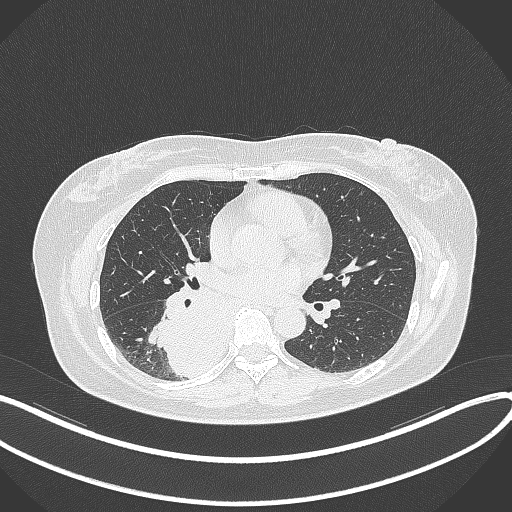
Chest CT, one axial slice; position 178 of 331 along the scan axis; reconstruction kernel B70f; 120 kVp; lung window (W 1500 / L -600 HU); 1 mm slice thickness; 512 × 512 image matrix, field of view 400 × 400 mm. Female patient, age 54 years. Case-level facts recorded for this patient, not image findings: clinical TNM (as recorded): T4 N0 M0.
Structures marked on this image (bounding box drawn by a radiologist):
- lung tumour (recorded histology: adenocarcinoma): box from (x=154, y=278) to (x=235, y=377) px